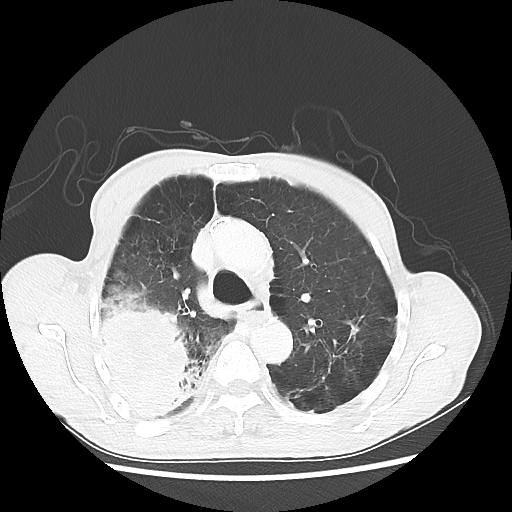
Chest CT, one axial slice. Position 38 of 58 along the scan axis. Lung window (W 1500 / L -600 HU). 512 × 512 image matrix. Patient: male, 75 years. From the clinical record (not read from this slice): clinical TNM (as recorded): T4 N1 M1.
Annotated regions visible in this slice (rectangle marked by the reading radiologist):
- lung tumour (recorded histology: adenocarcinoma): bounding box [x1, y1, x2, y2] px = [89, 289, 203, 421]